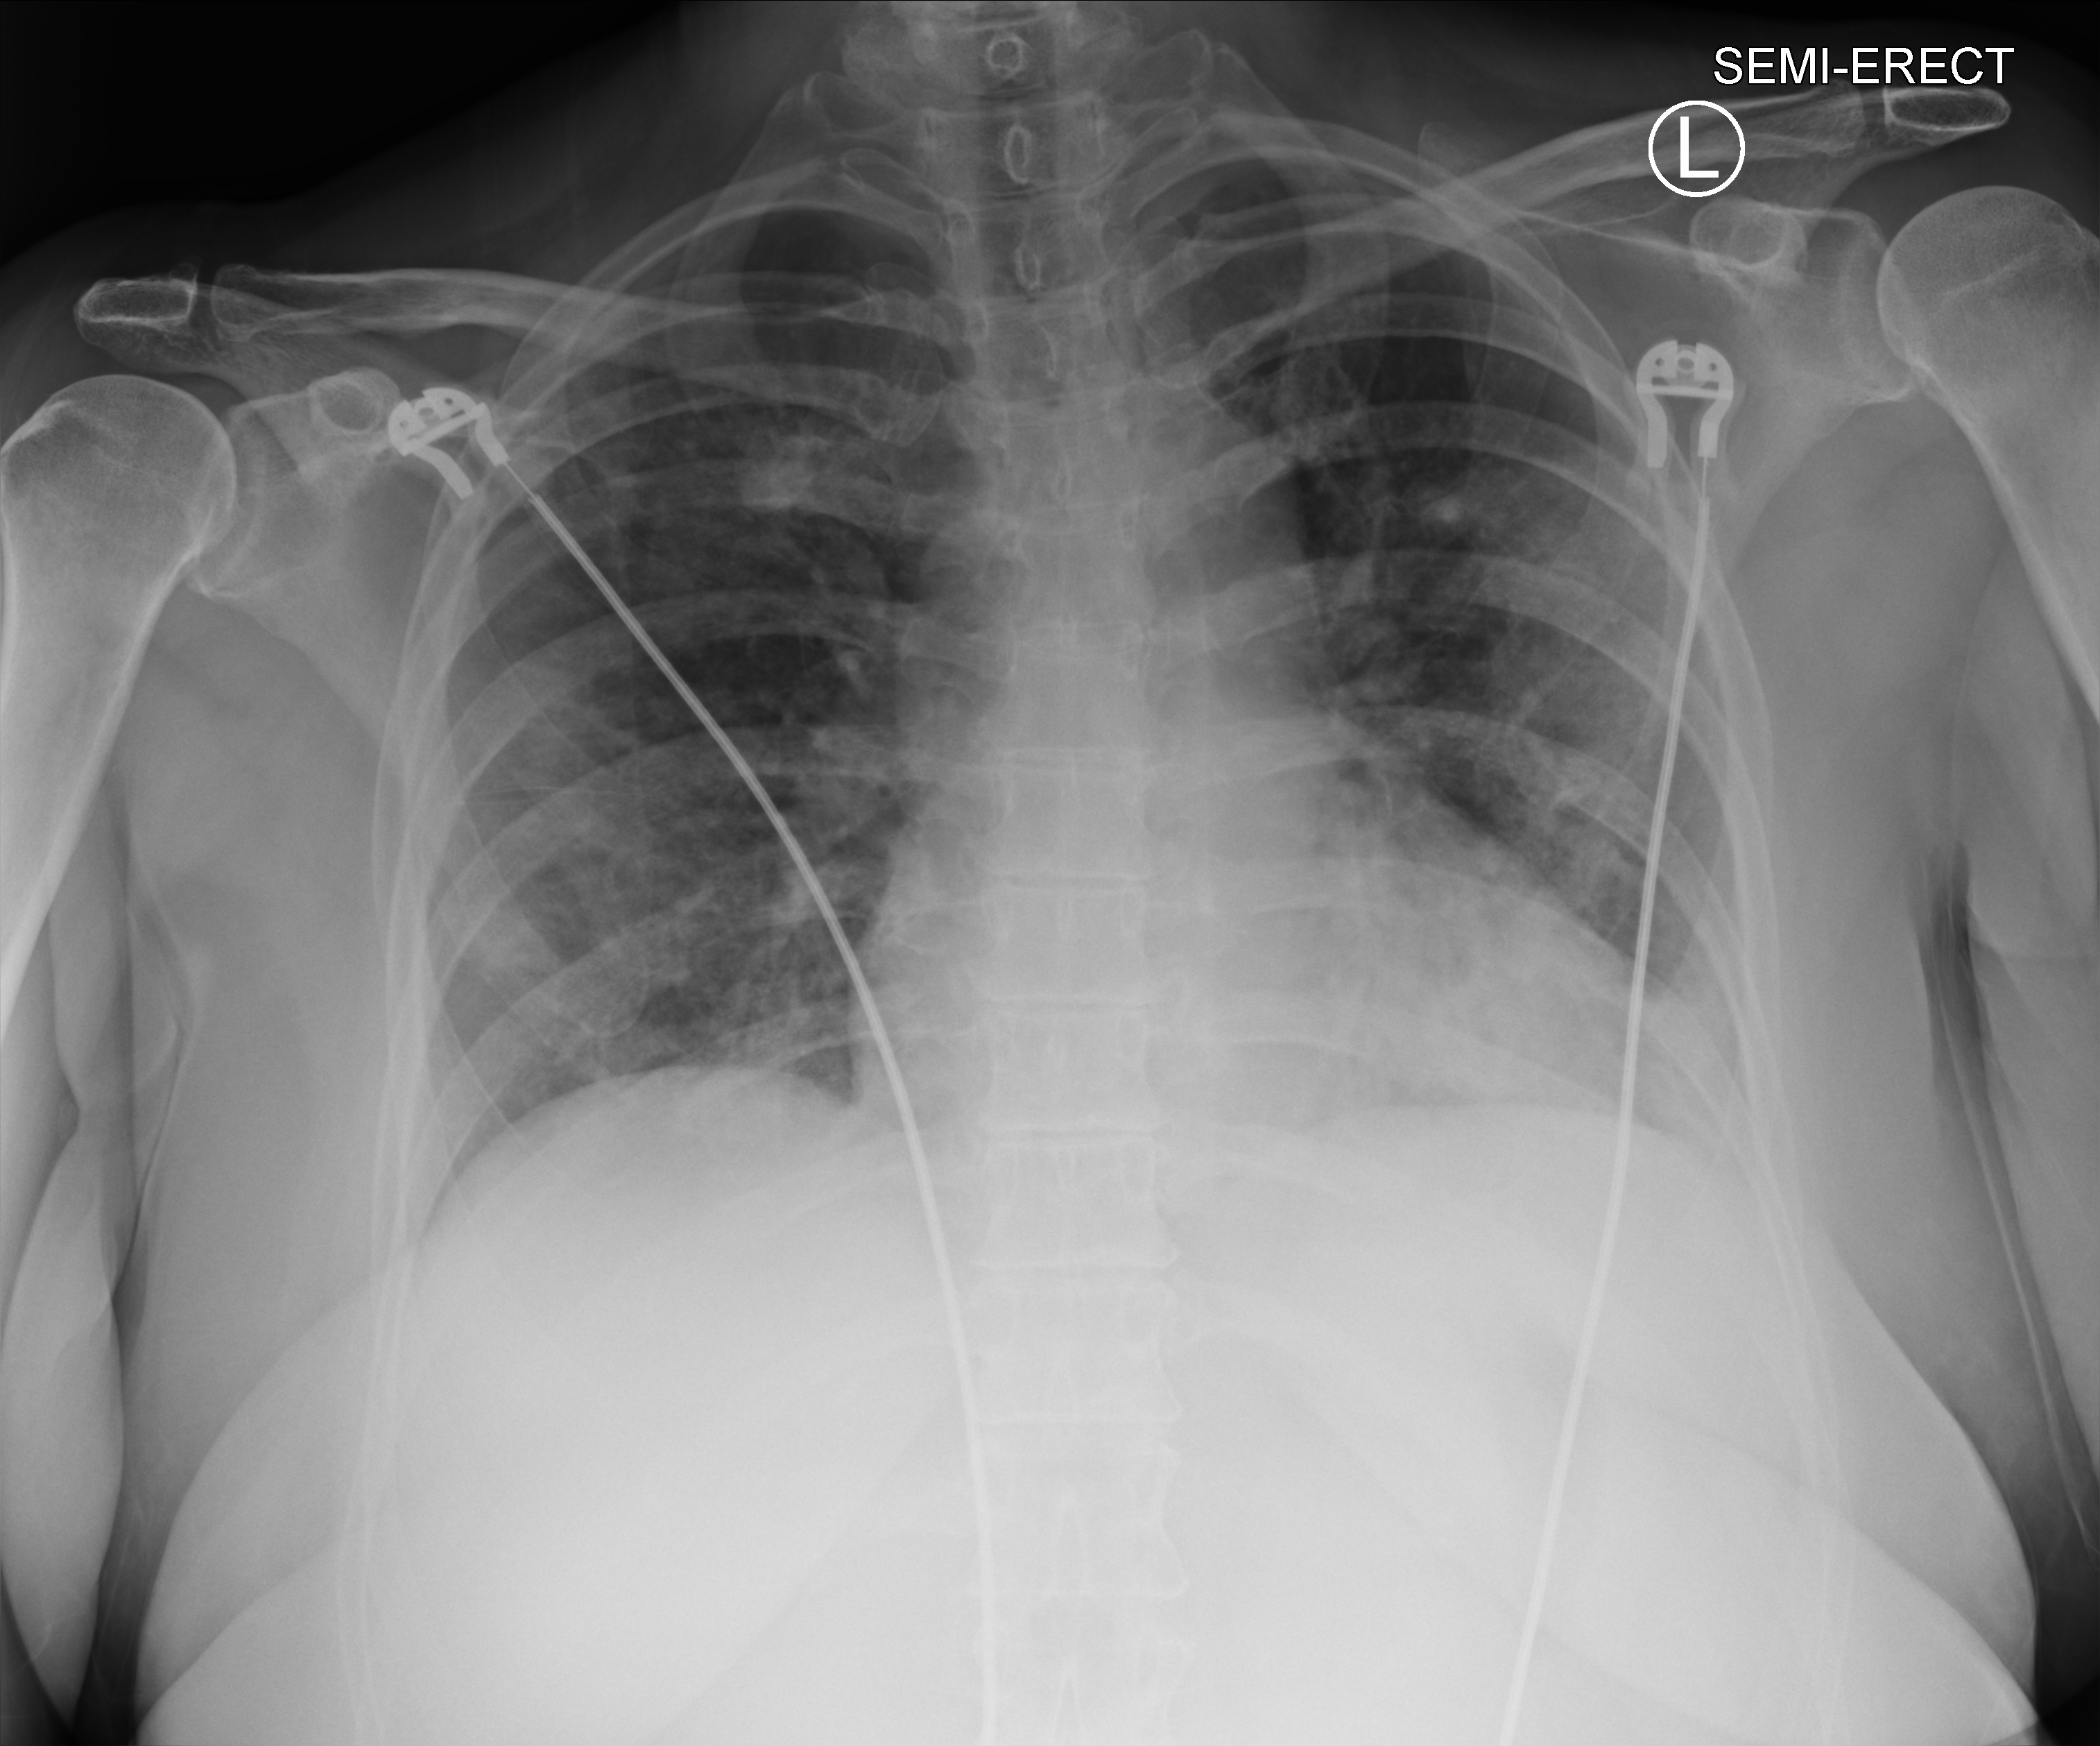
Portable chest radiograph, anteroposterior (AP) projection. Female patient hospitalised with COVID-19, age 18–59 years.
From the hospital-stay record, not from the radiograph (when in the stay this image was taken is not recorded): mechanically ventilated during this hospital stay: yes.